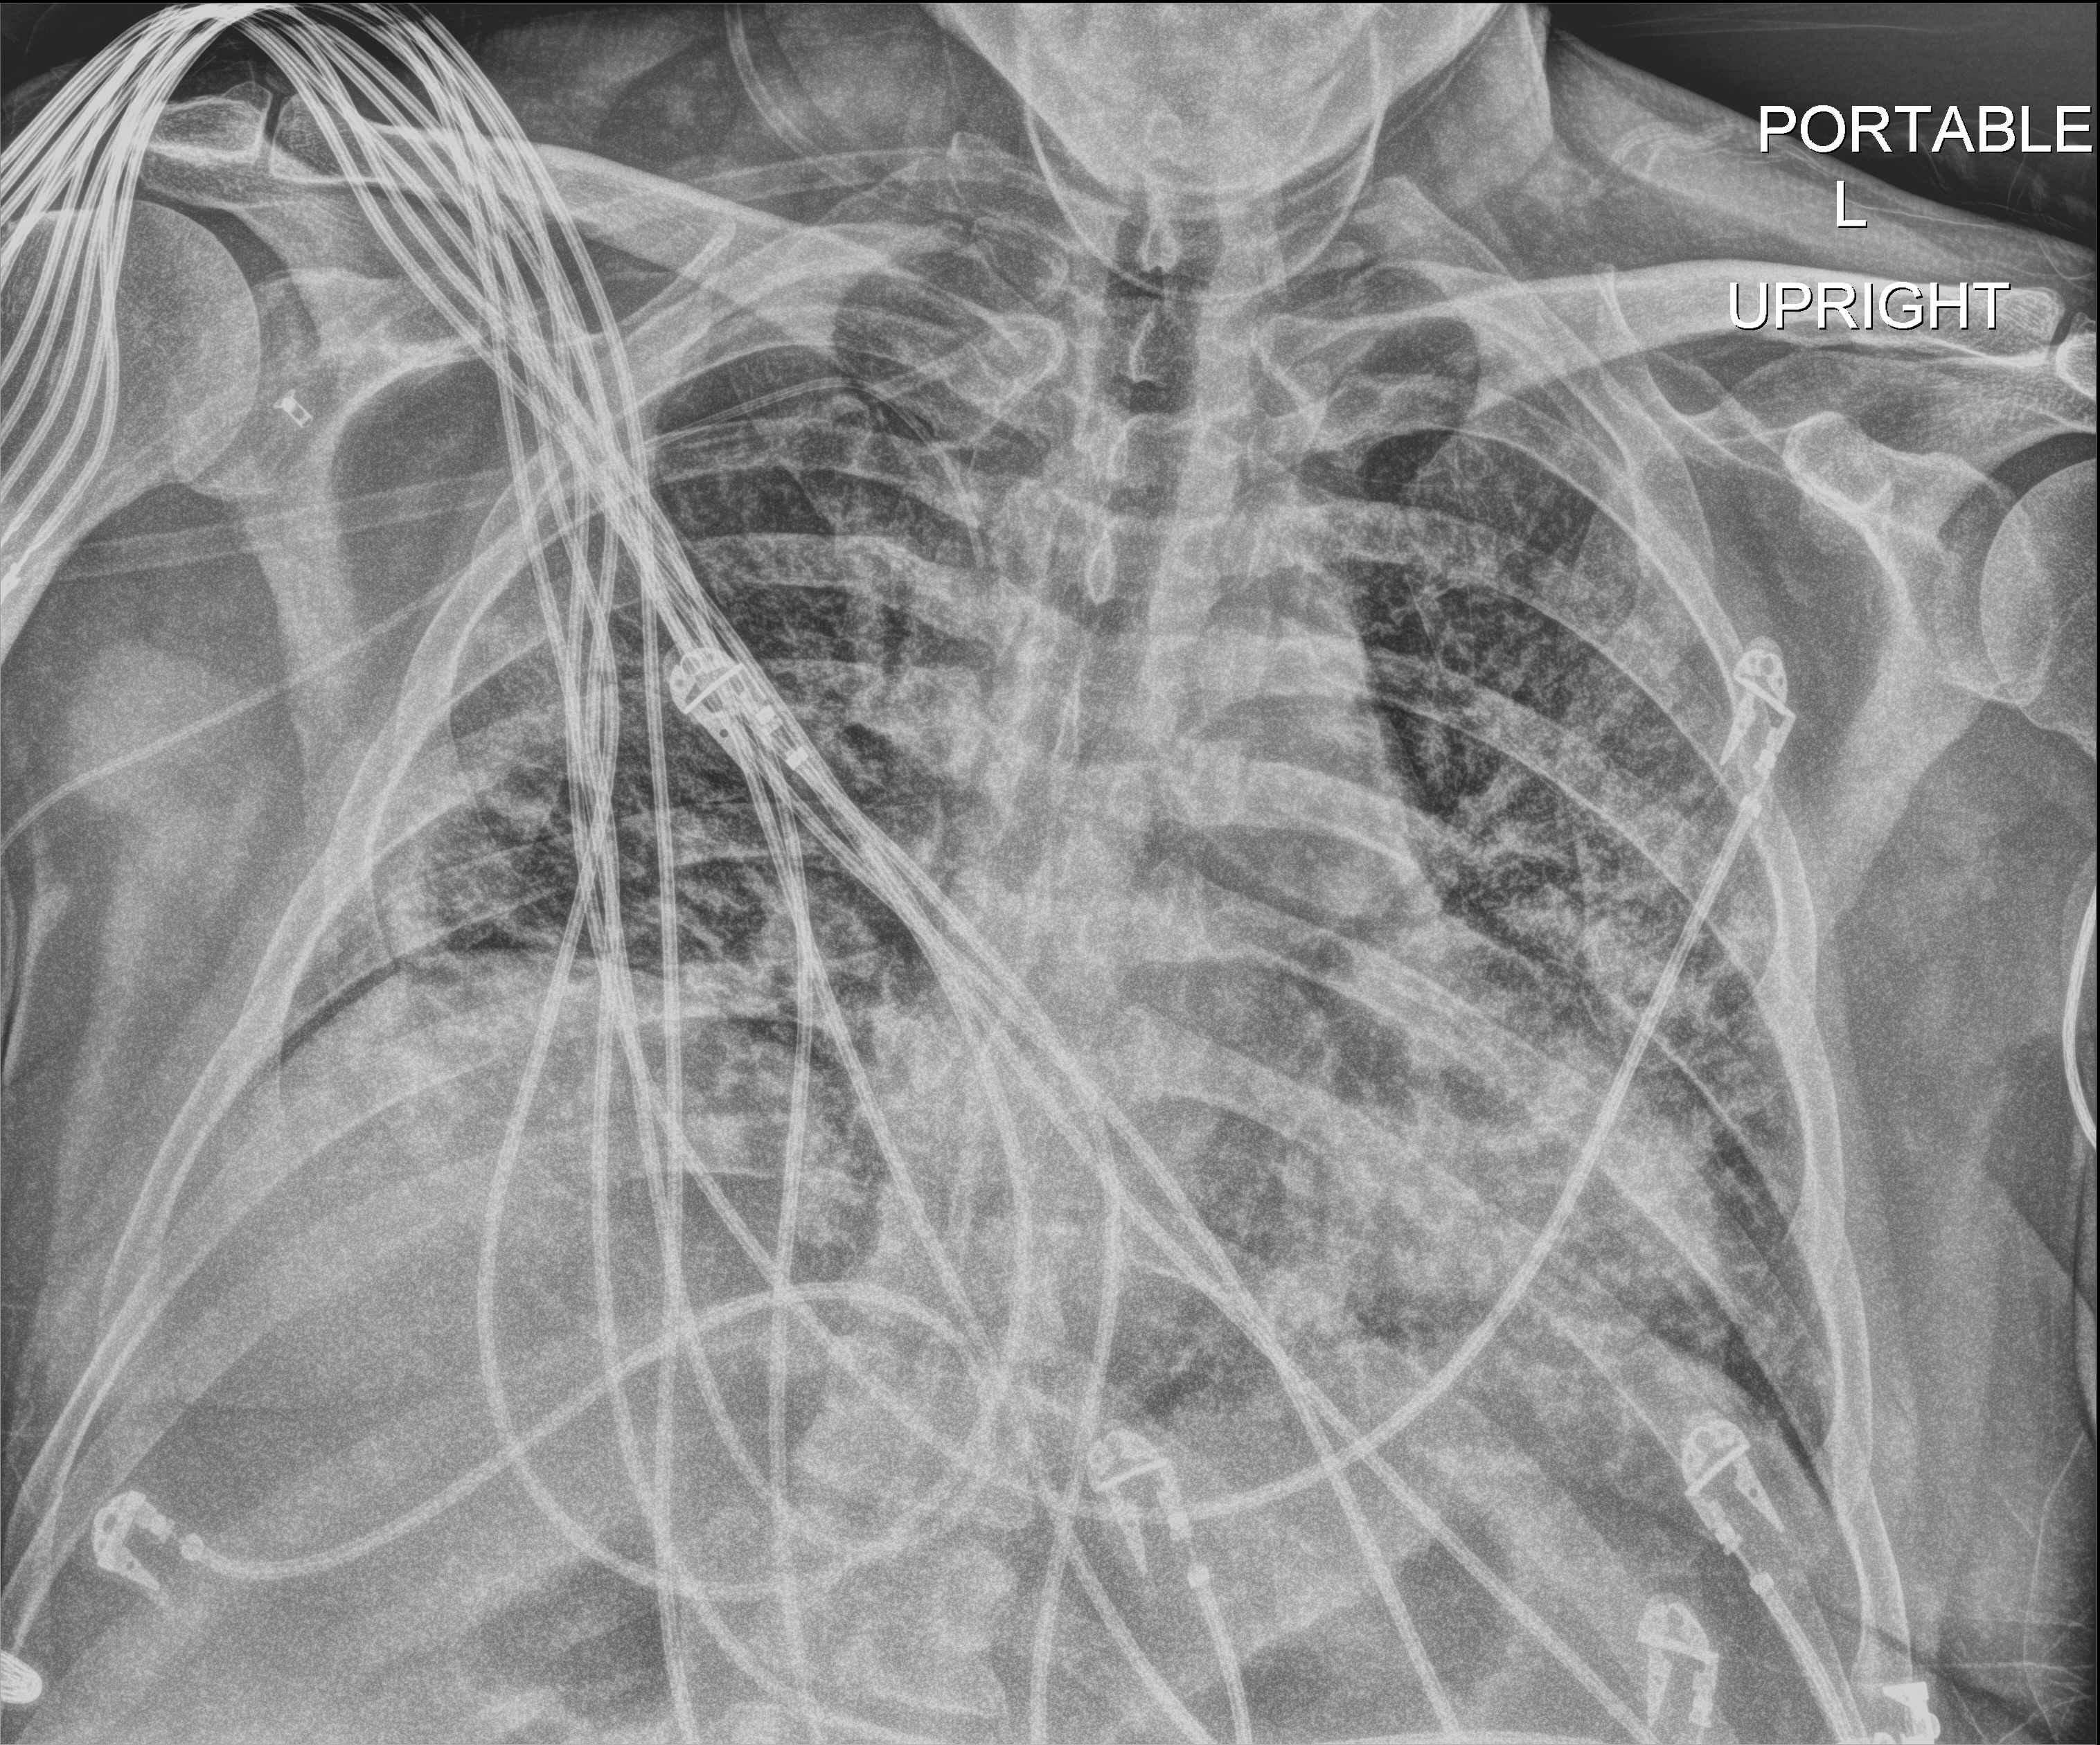
Portable chest radiograph, anteroposterior (AP) projection. Male patient hospitalised with COVID-19, age 18–59 years.
Hospital-stay facts (about this admission, not read from this image; timing relative to this image not recorded):
- mechanically ventilated during this hospital stay: yes
- COPD (admission record): no